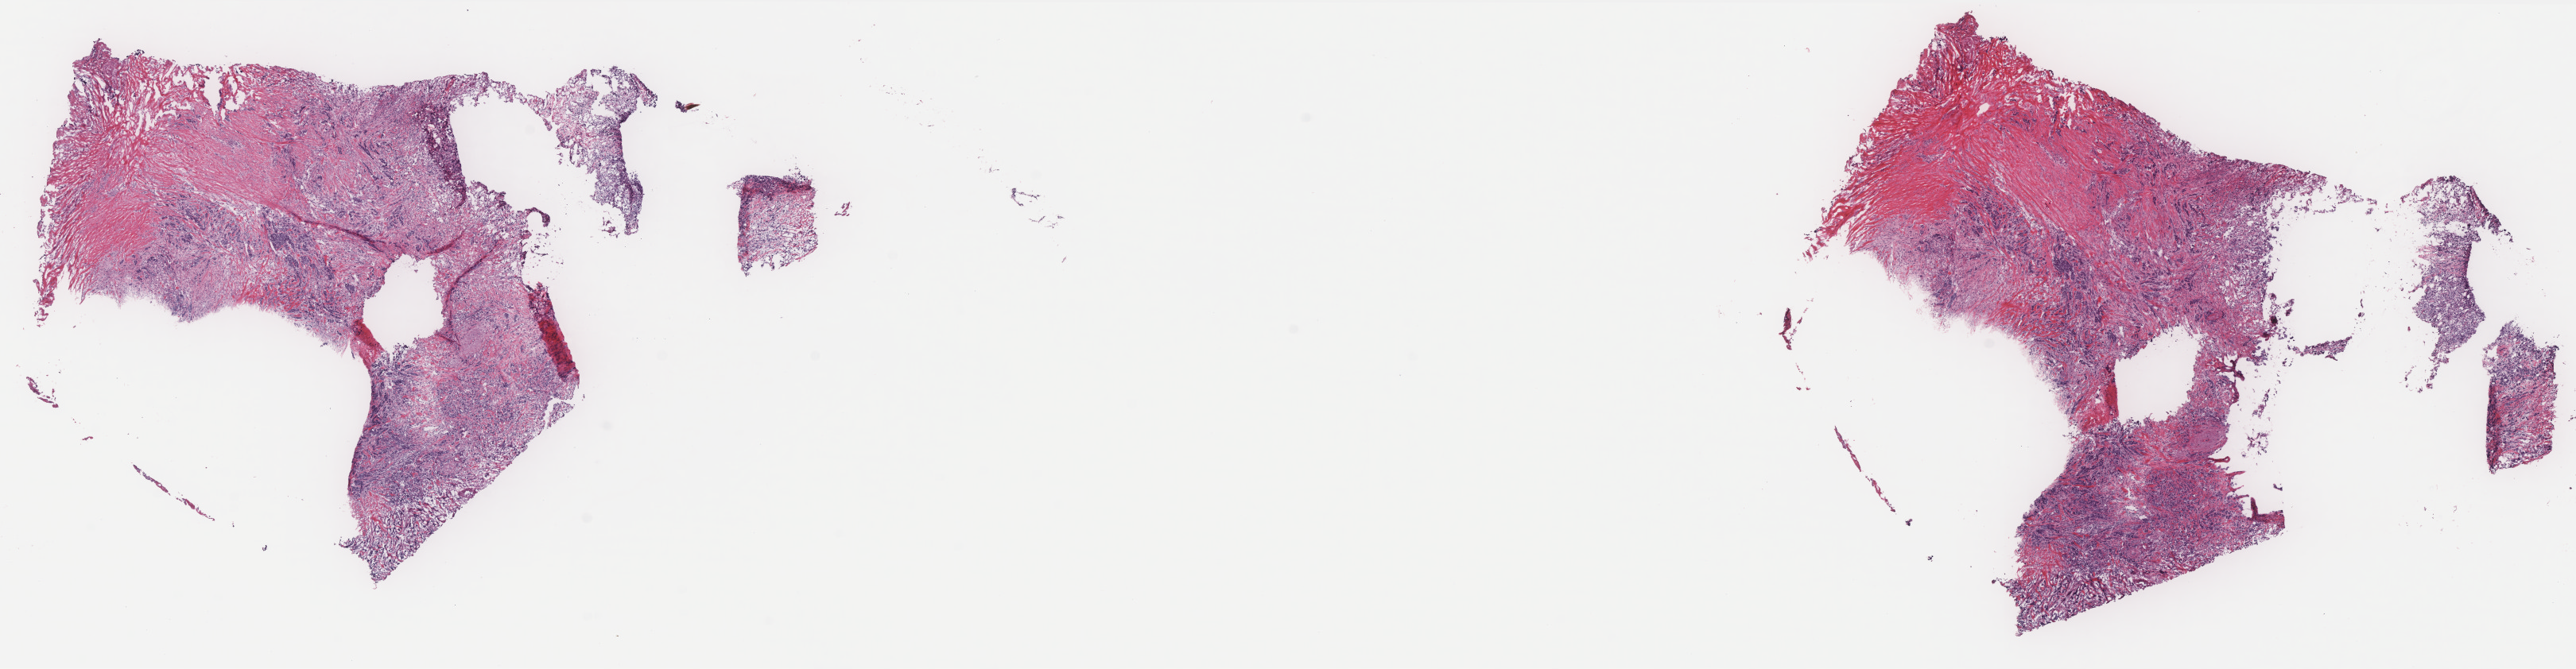
Whole-slide histology image, H&E — low-resolution overview of the scanned area, about 26.0 x 6.8 mm, frozen section from the top of the tissue portion, primary tumour sample from the breast. Female patient; age at initial diagnosis 68 years. Composition of this section per pathologist review: tumour cells 100%, tumour nuclei 80%, normal cells 0%, stromal cells 0%, necrosis 0%. Infiltration values recorded for this section: lymphocyte infiltration 0%, monocyte infiltration 0%, neutrophil infiltration 0%.
- histologic diagnosis: Infiltrating duct carcinoma, NOS
- laterality: right
- AJCC pathologic stage: IIIA (7th edition)
- lymph nodes positive (case pathology): 1 of 15 examined
- TNM: T2 N2 M0